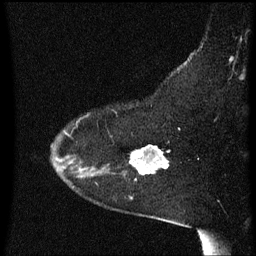
Breast MRI (dynamic contrast-enhanced), one sagittal slice. Dynamic contrast-enhanced series, image 2 of 3 at this slice position (ordered by acquisition). 1.5 T. TE 4.2 ms, TR 8.4 ms. 256 × 256 image matrix. Patient: female, 54 years. From the clinical record (not read from this slice): setting: breast cancer imaged before/during neoadjuvant chemotherapy; receptor status: HR-positive, HER2-negative.
Outlined on this slice (semi-automatic segmentation, software-assisted and operator-edited):
- analysis volume of interest (the breast-tissue region the enhancement analysis was run in; not a lesion): bounding box (x1, y1, x2, y2) in pixels: (121, 146, 170, 181)
- tumour enhancement mask (voxels above the 70 % enhancement threshold inside the analysis volume of interest): (131, 146, 170, 175)